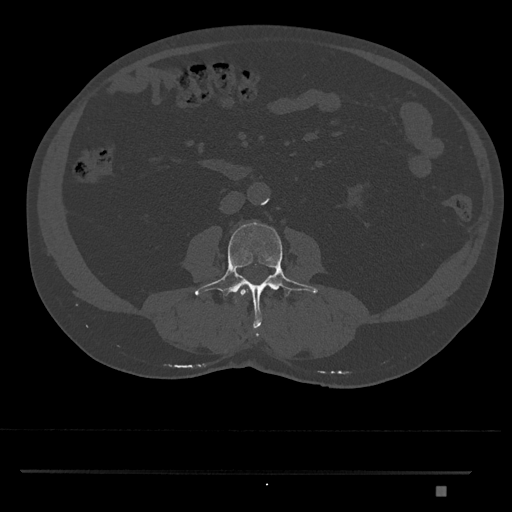
CT including the spine, one axial slice. Position 685 of 1134 along the scan axis. 120 kVp. Bone window (W 1800 / L 400 HU). 0.5 mm slice thickness. 512 × 512 image matrix, field of view 429 × 429 mm. Patient: male, 65 years. Case-level facts recorded for this patient, not image findings: primary cancer: prostate.
Structures marked on this image (semi-automatically segmented with operator editing):
- L2 vertebra: bounding box <240,288,248,297> (left, top, right, bottom; pixels)
- L3 vertebra: <195,221,318,337>